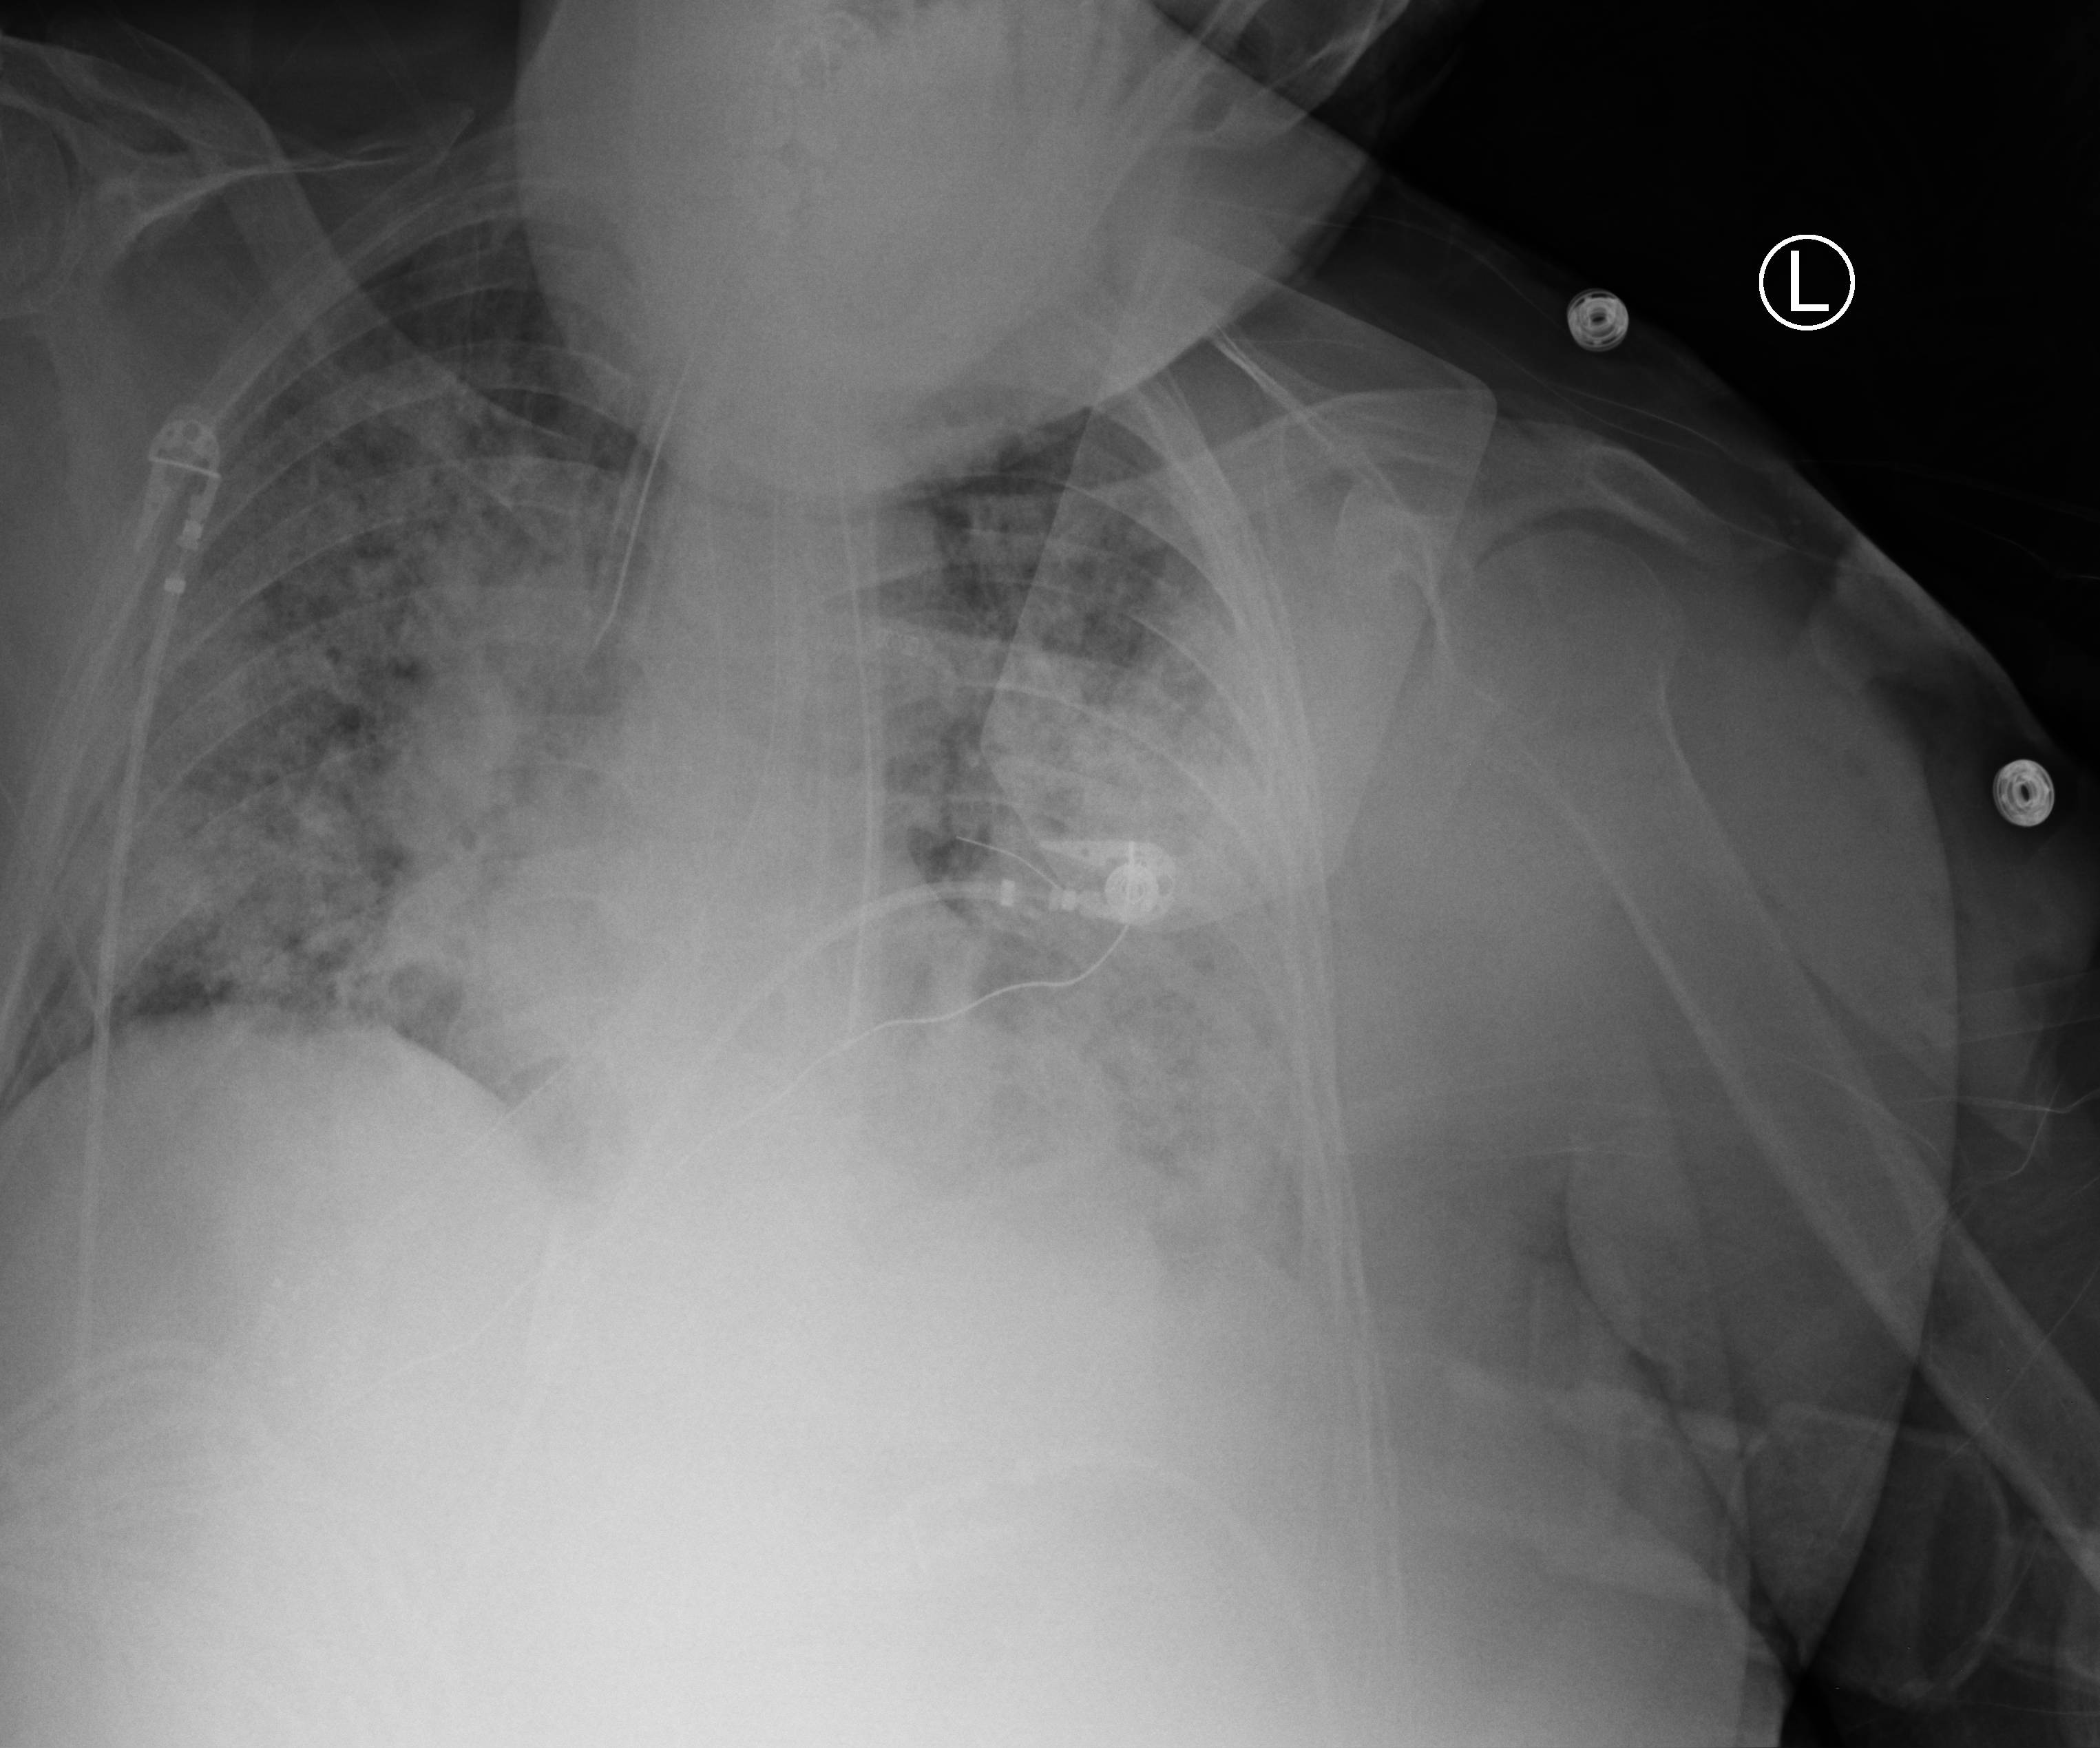
Chest X-ray (portable); anteroposterior (AP) projection. Patient hospitalised with COVID-19; female, aged 60–74 years.
From the hospital-stay record, not from the radiograph (when in the stay this image was taken is not recorded): admitted to intensive care during this hospital stay: yes.